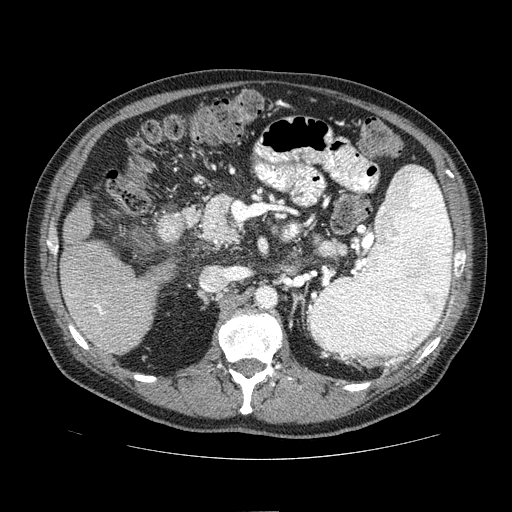
Contrast-enhanced abdominal CT (liver protocol), one axial slice. Position 28 of 81 along the scan axis. Reconstruction kernel STANDARD. 100 kVp. One of 2 acquisitions stored at this slice position. Soft-tissue window (W 400 / L 40 HU). 2.5 mm slice thickness. 512 × 512 image matrix, field of view 400 × 400 mm. Case-level facts recorded for this patient, not image findings: diagnosis: hepatocellular carcinoma (patient treated with transarterial chemoembolisation; whether this scan precedes or follows treatment is not stated here); TNM stage (as recorded): Stage-IIIA.
Annotated regions visible in this slice (semi-automatically segmented with operator editing):
- liver parenchyma outside the tumour (the mass and vessels are separate outlines, so this box may not span the whole liver): bounding box [x1, y1, x2, y2] px = [60, 202, 174, 354]
- liver vessels: [68, 290, 130, 315]